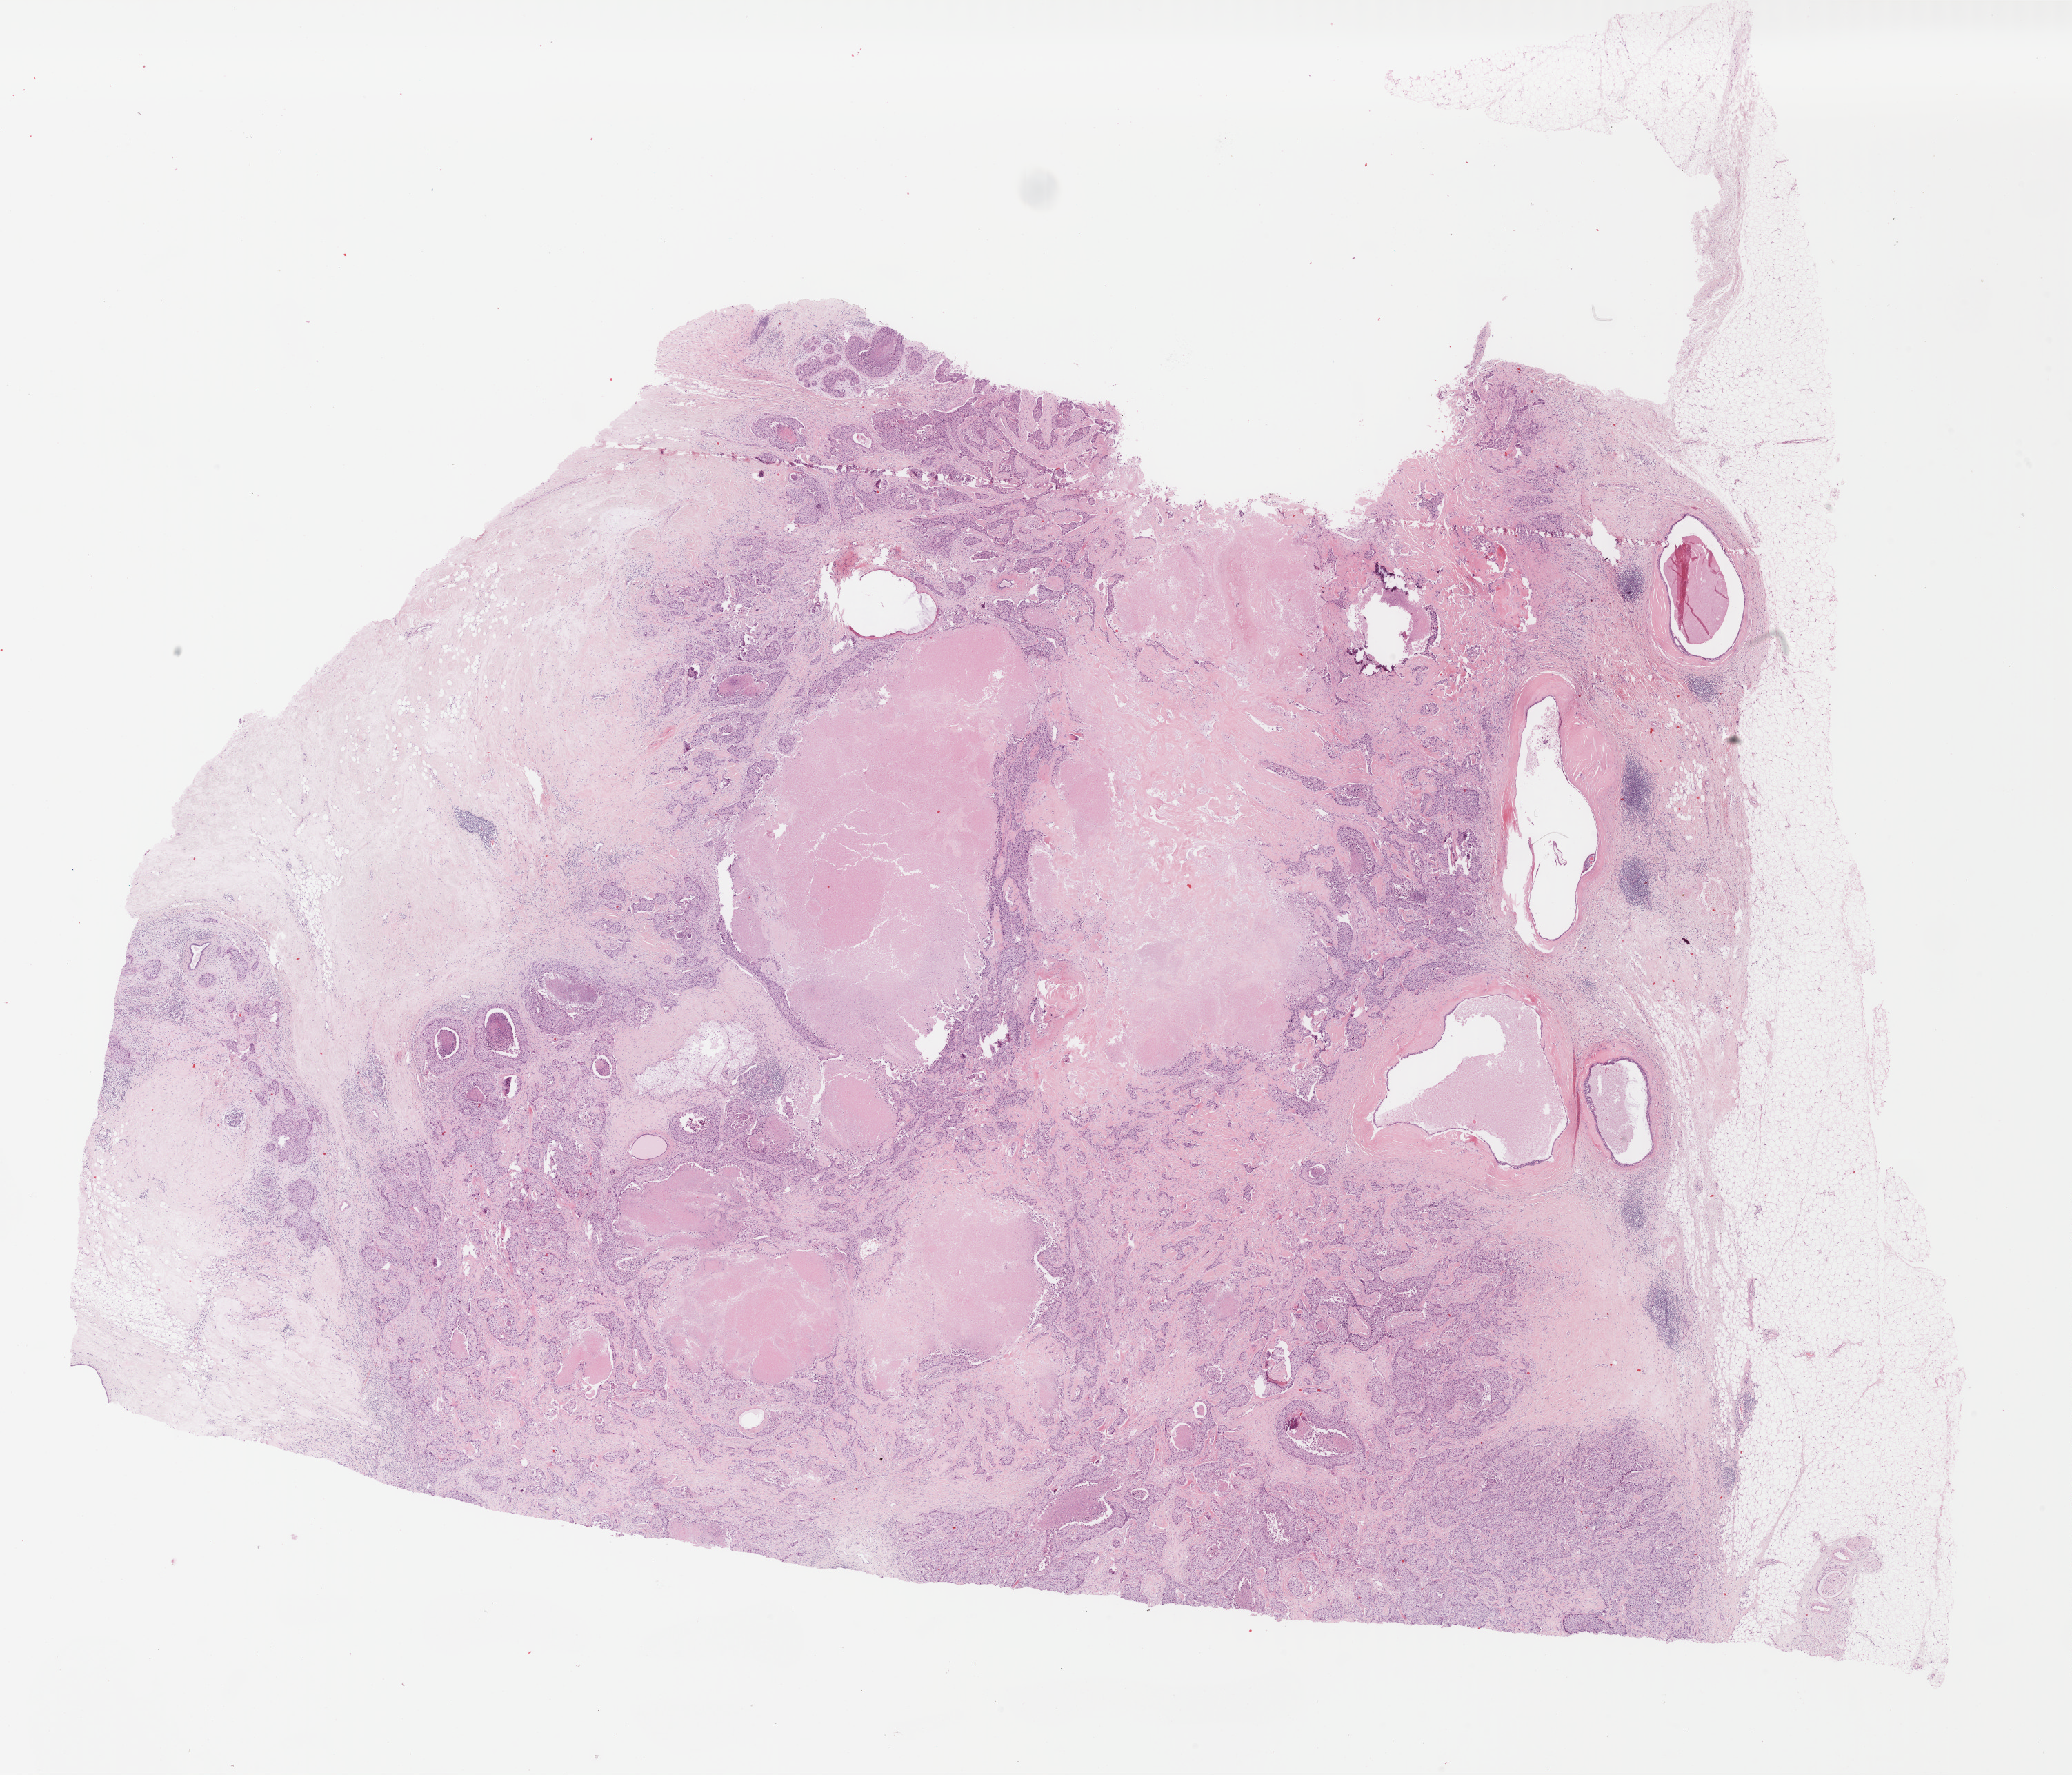
Whole-slide histology image, H&E — shown as a low-resolution overview of the whole scanned area (about 23.8 x 20.4 mm, from a 40x scan). Formalin-fixed paraffin-embedded (FFPE) diagnostic section. Breast, primary tumour sample. Female, age 51 years at initial diagnosis.
* lymph nodes positive (case pathology): 9 of 11 examined
* diagnosis: Infiltrating duct carcinoma, NOS
* laterality: right